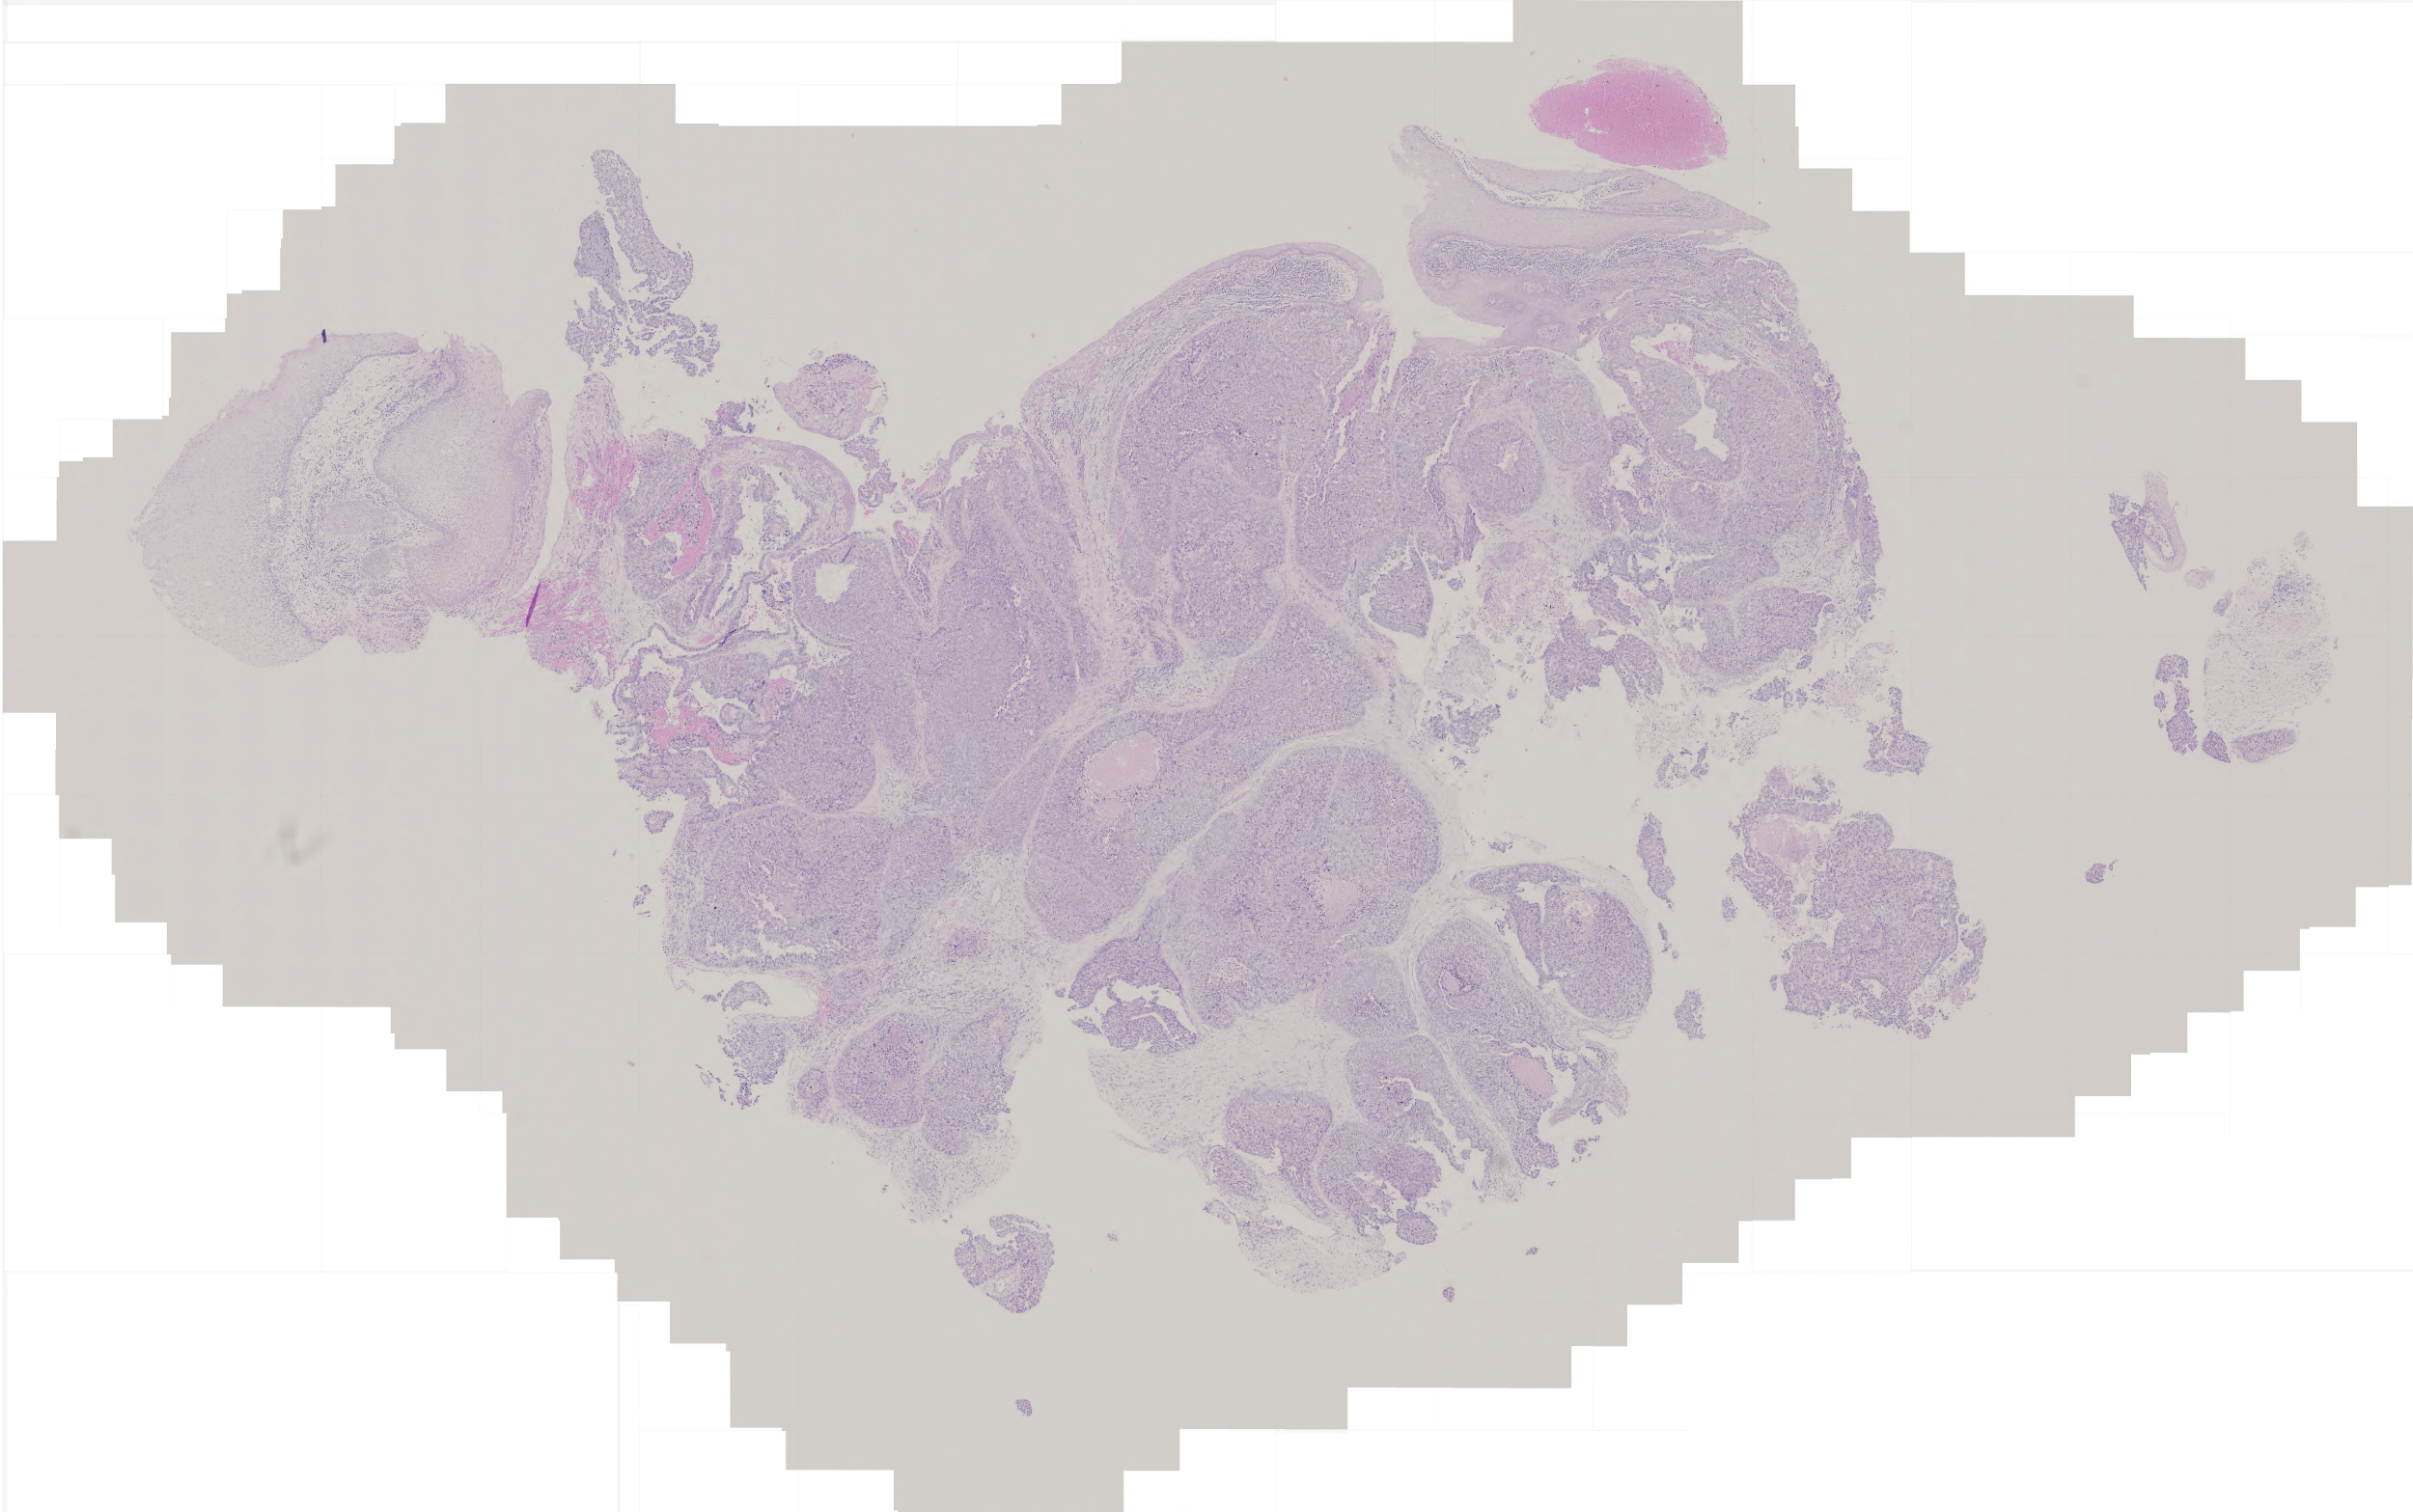
Digitized Hematoxylin and eosin (H&E) stained tissue section (whole slide), low-resolution overview of the scanned area, about 5.0 x 3.1 mm; formalin-fixed paraffin-embedded (FFPE) diagnostic section; primary tumour sample from the stomach. Male, age 72 years at initial diagnosis. Histologic grade: G3 (poorly differentiated).
Lymph nodes positive (case pathology): 0 of 23 examined. Histologic diagnosis: Adenocarcinoma, NOS (cardia, NOS). AJCC pathologic stage: IB. TNM: T2 N0 M0.